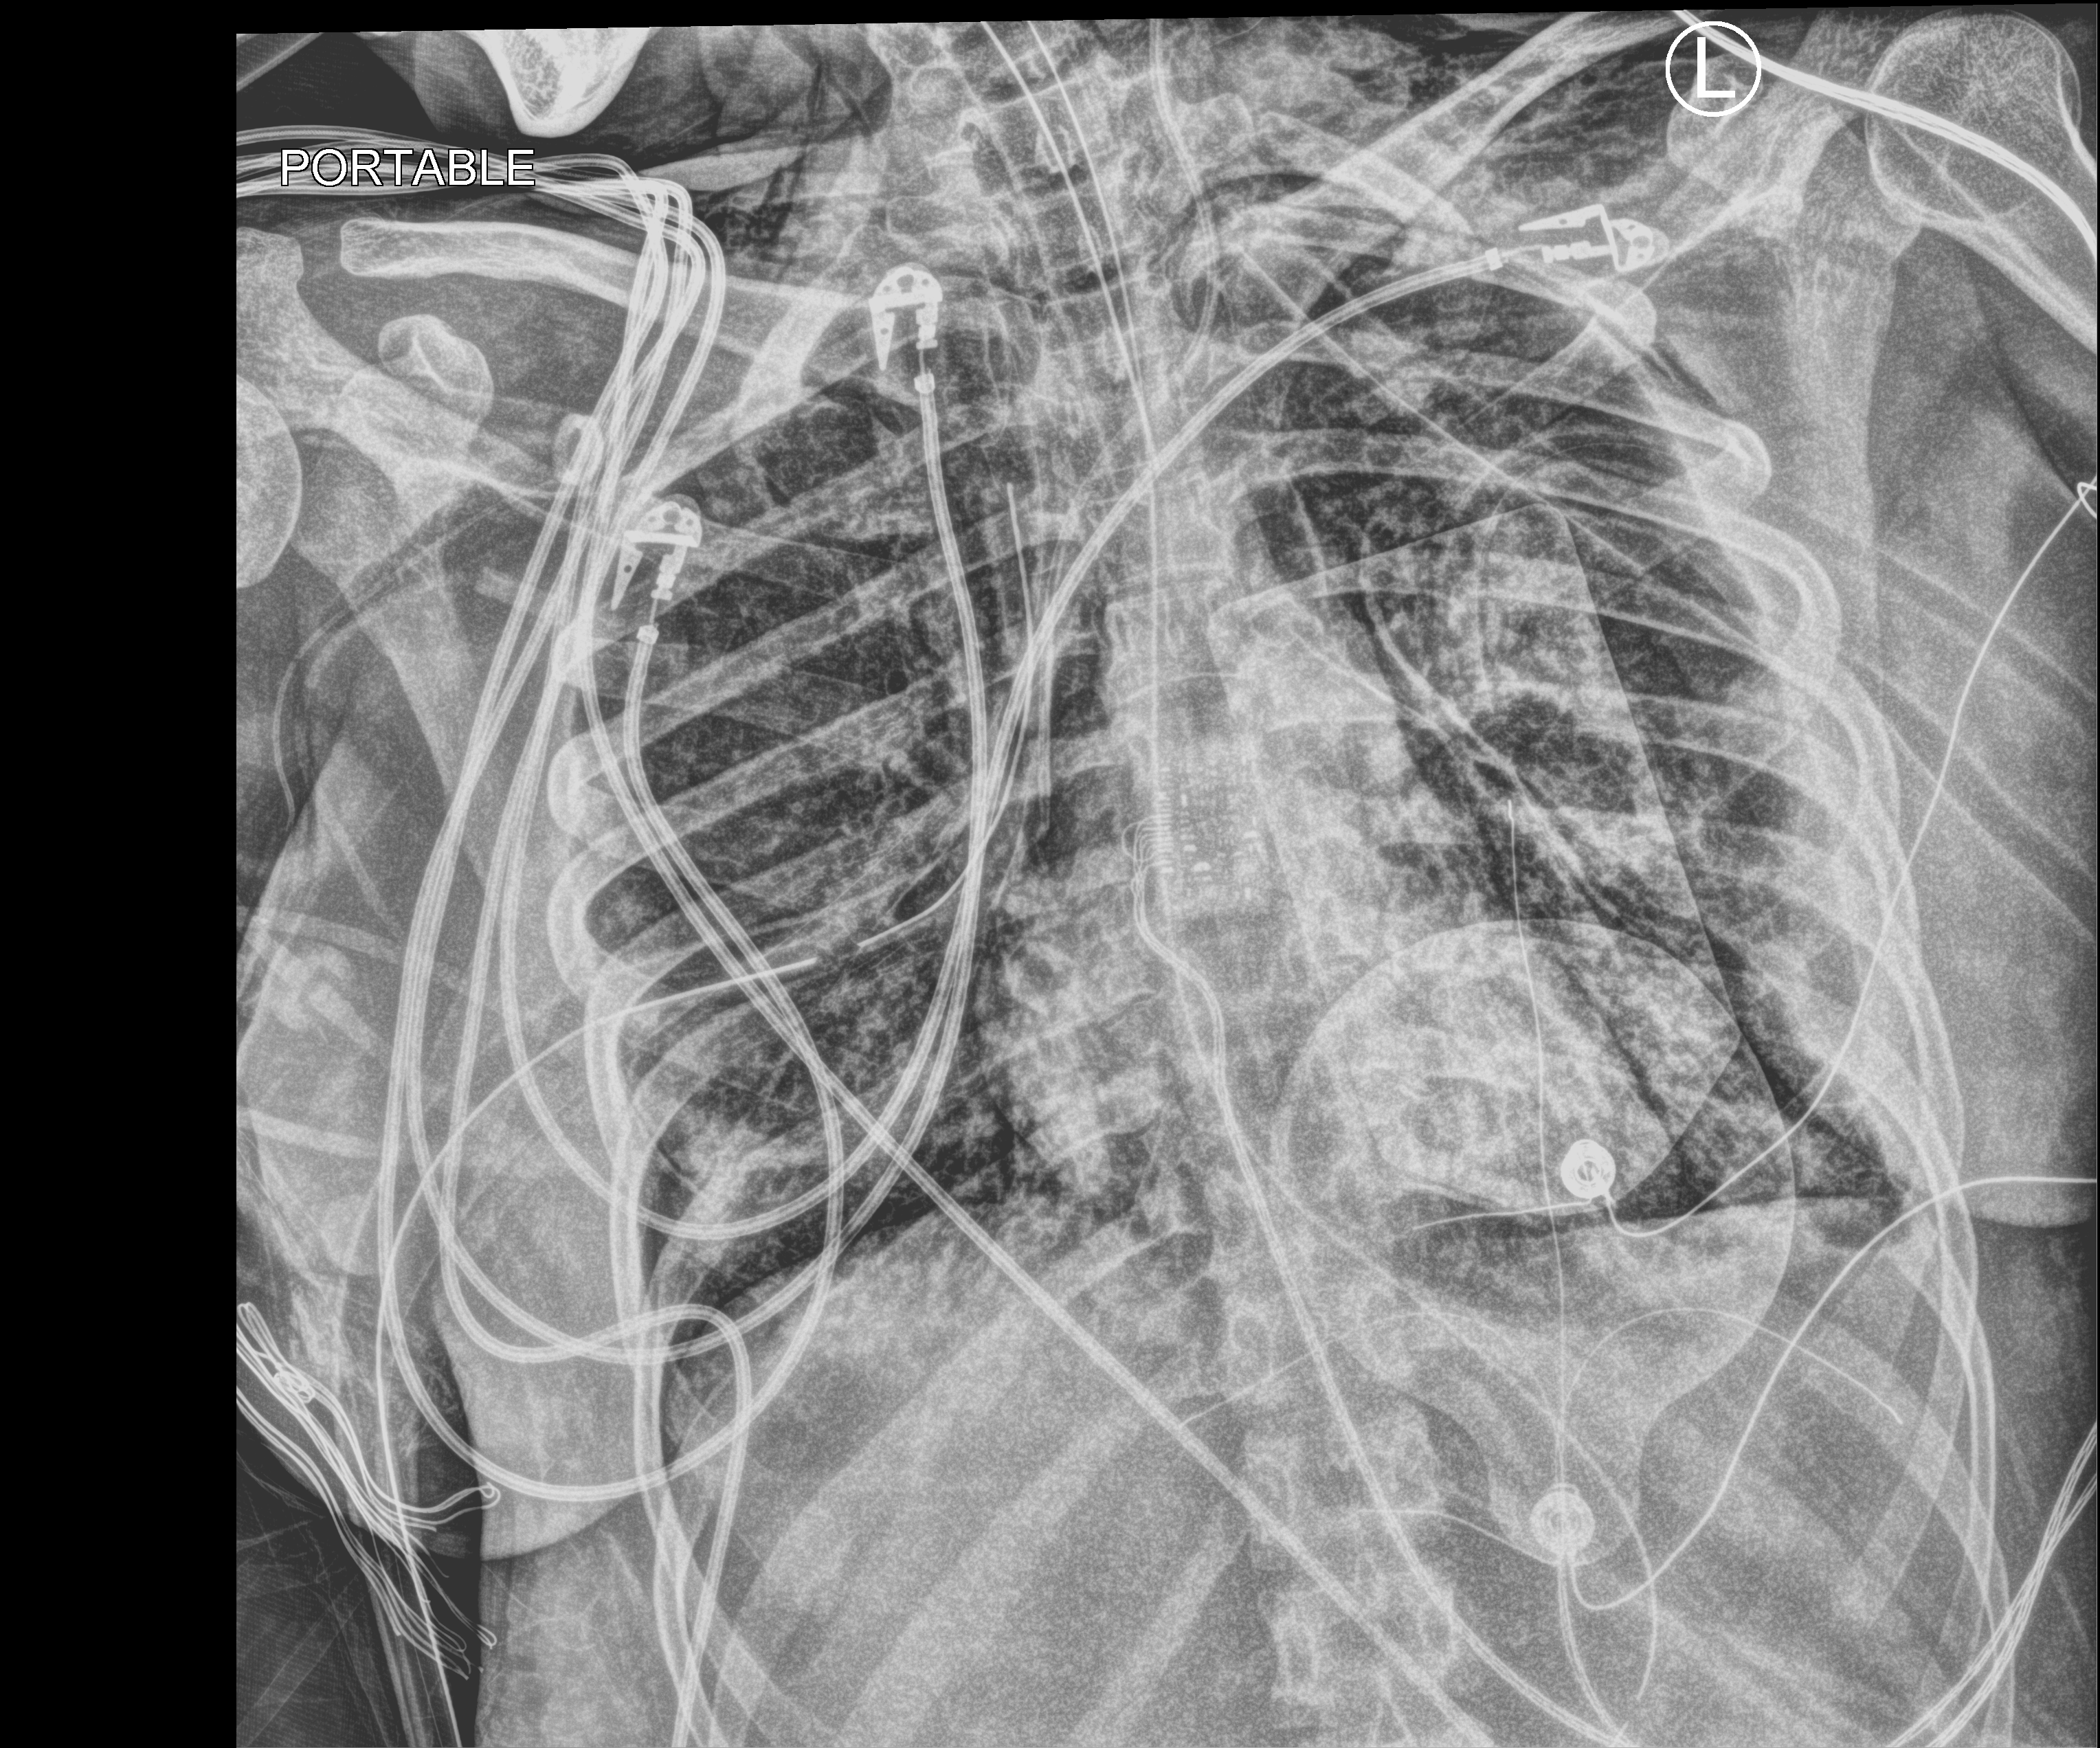
Portable chest radiograph. Adult patient hospitalised with COVID-19, age 18–59 years.
Admission-level facts for this patient (not findings on this image; timing relative to this image not recorded): admitted to intensive care during this hospital stay: yes.